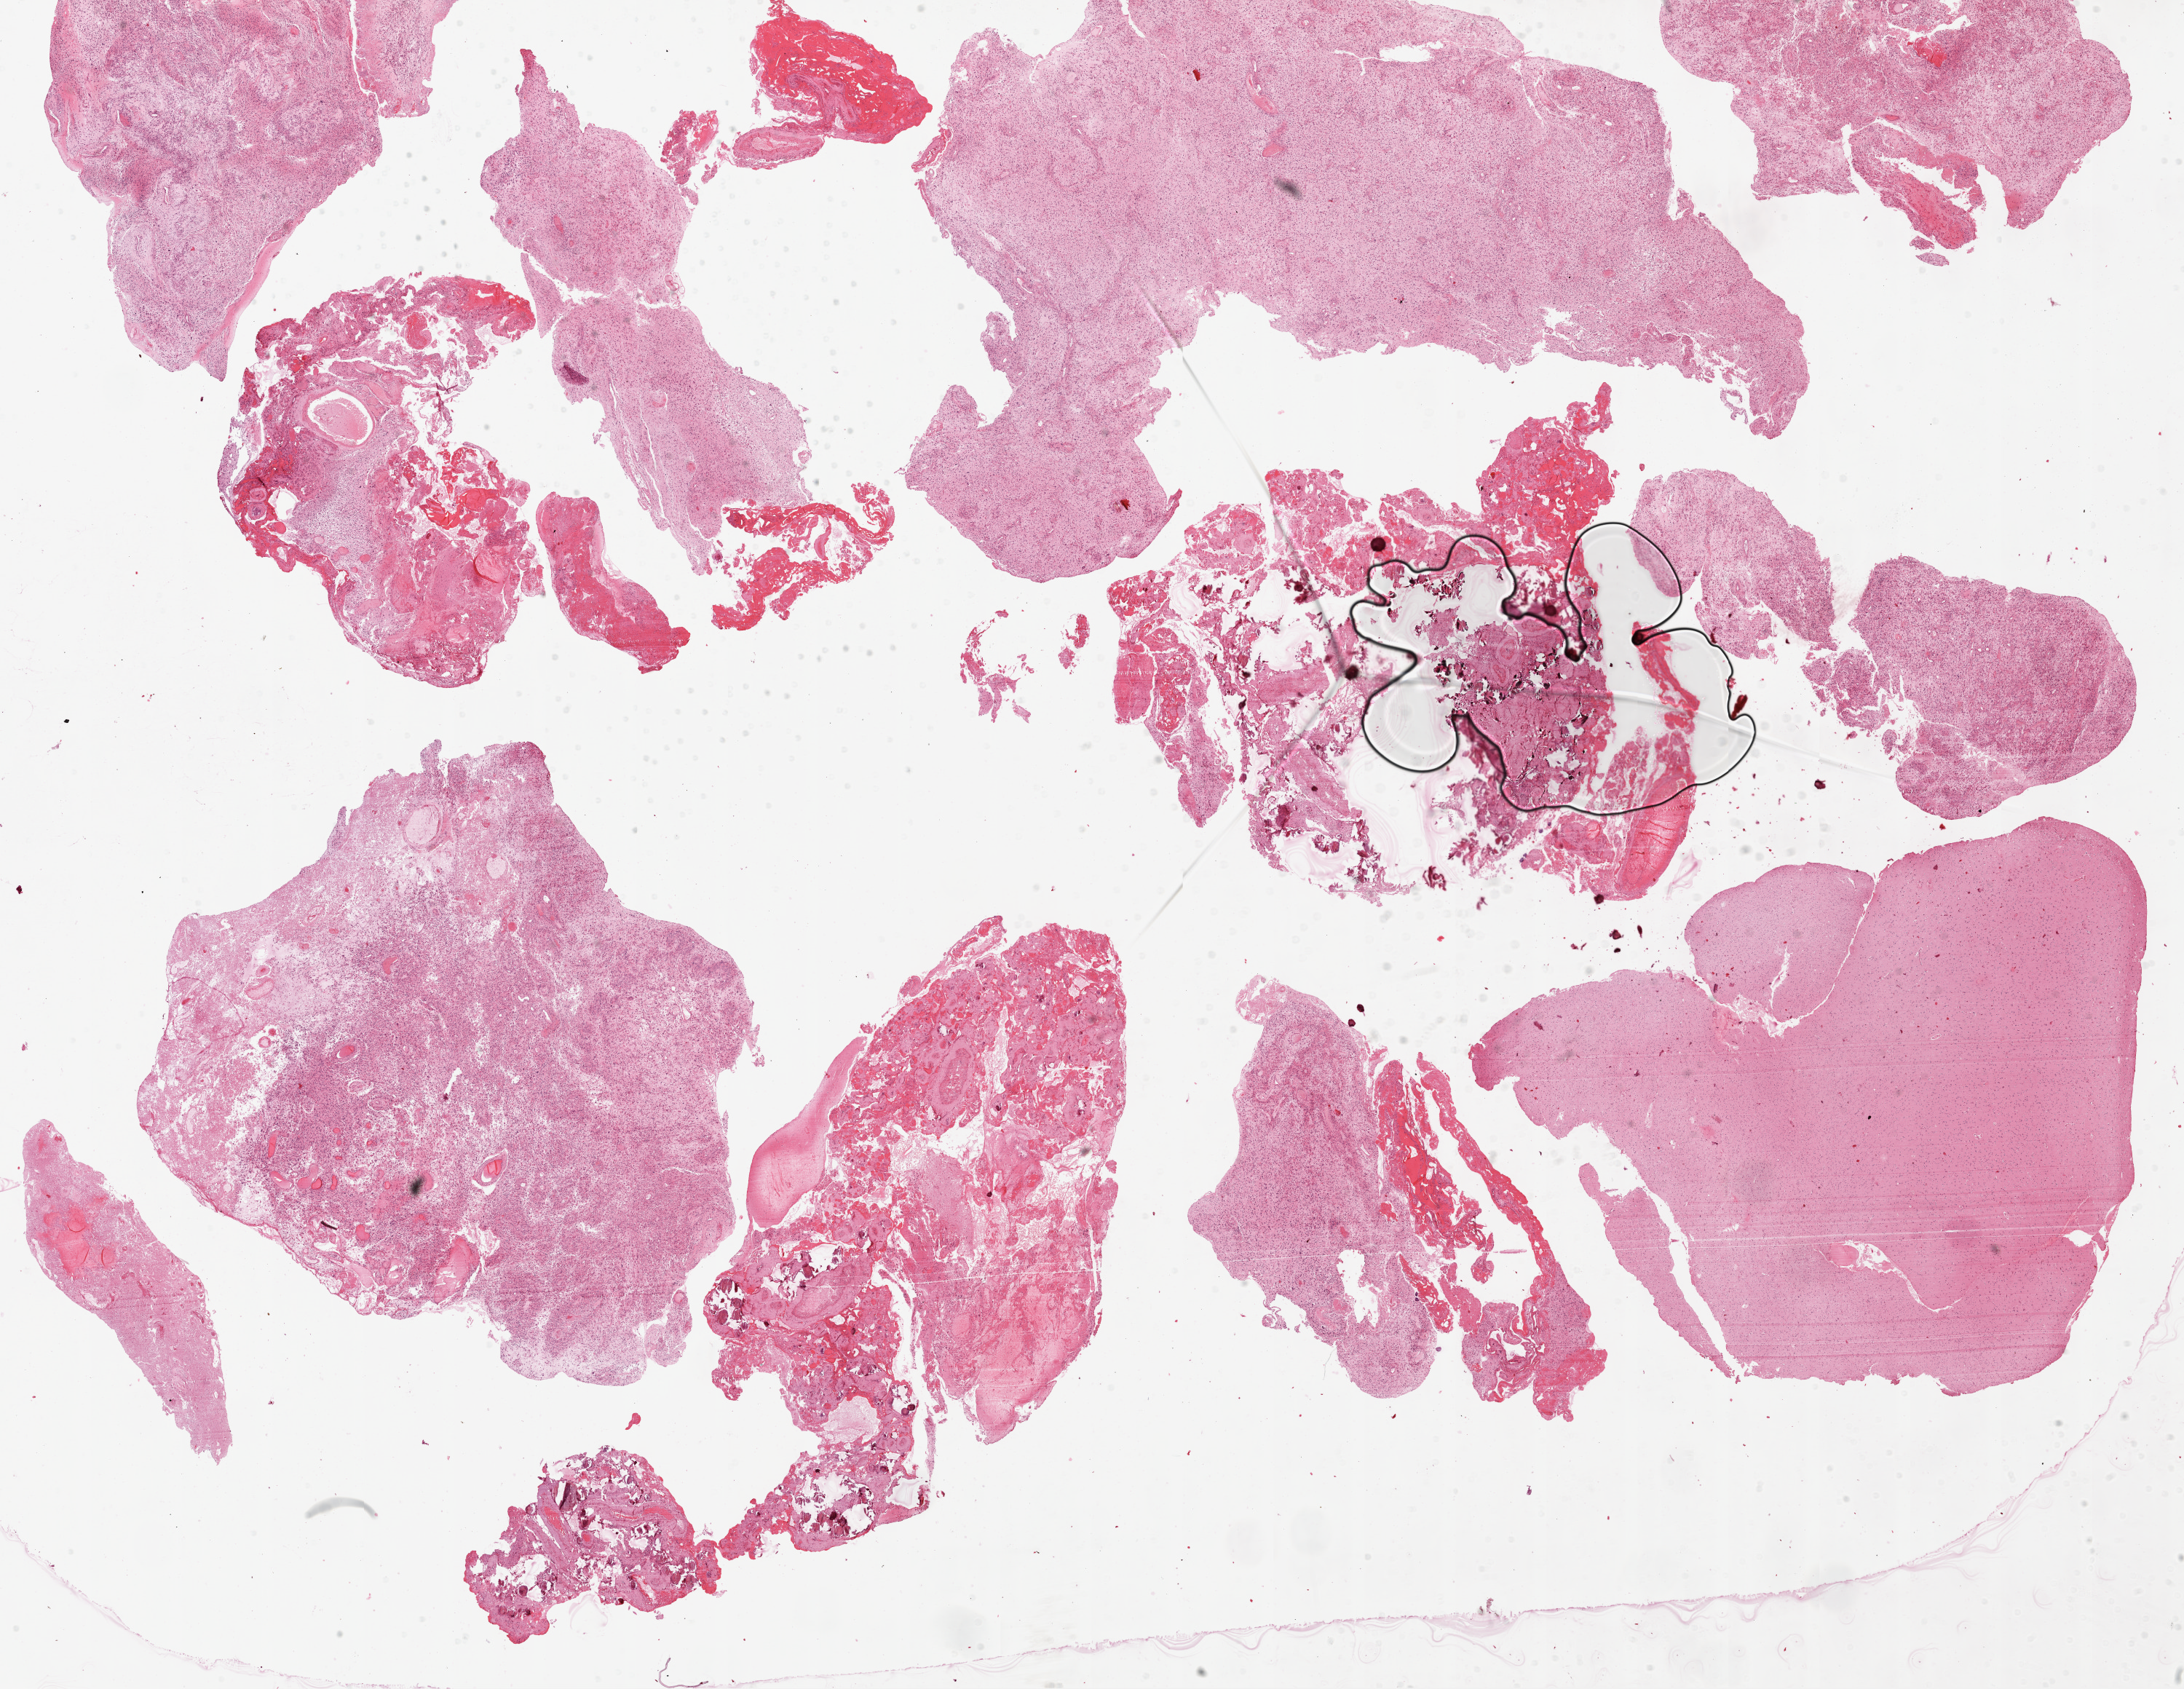
Digitized H&E tissue section (whole slide), low-resolution overview of the scanned area, about 24.1 x 18.6 mm (slide scanned at 20x); formalin-fixed paraffin-embedded (FFPE) diagnostic section; brain, primary tumour sample. Male, age 57 years at initial diagnosis.
- histologic diagnosis: Glioblastoma